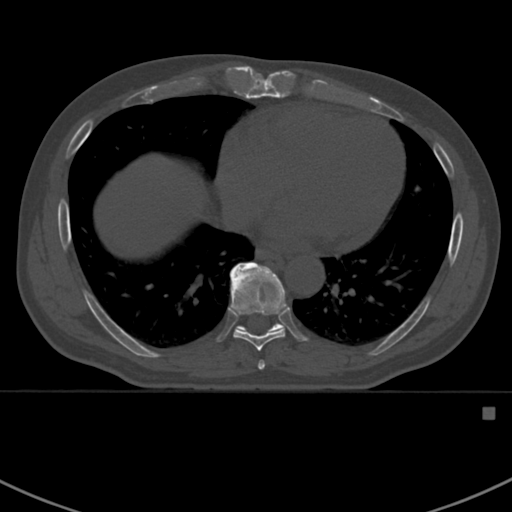
CT including the spine, one axial slice. Position 396 of 412 along the scan axis. Bone window (W 1800 / L 400 HU). 1.5 mm slice thickness. 512 × 512 image matrix, field of view 358 × 358 mm. Patient: male, 59 years. Case-level facts recorded for this patient, not image findings: primary cancer: prostate.
Outlined on this slice (semi-automatically segmented with operator editing):
- T7 vertebra: bounding box [x1, y1, x2, y2] px = [257, 360, 265, 370]
- T8 vertebra: [228, 266, 285, 351]
- T9 vertebra: [230, 262, 288, 333]